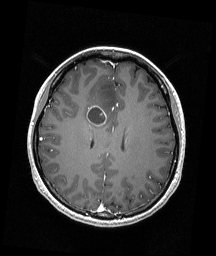
Brain MRI from a brain-tumour surgery series, one axial slice. Slice 72 of 192 in the series (ordered by position). T1-weighted post-contrast. 1 mm slice thickness. 216 × 256 image matrix, field of view 211 × 250 mm. Case-level facts recorded for this patient, not image findings: histopathology: Astrocytoma; WHO grade: 4; IDH mutation: yes; tumour location: Right Frontal.
Outlined on this slice (expert manual segmentation):
- tumour: bounding box [x1, y1, x2, y2] px = [85, 105, 107, 126]